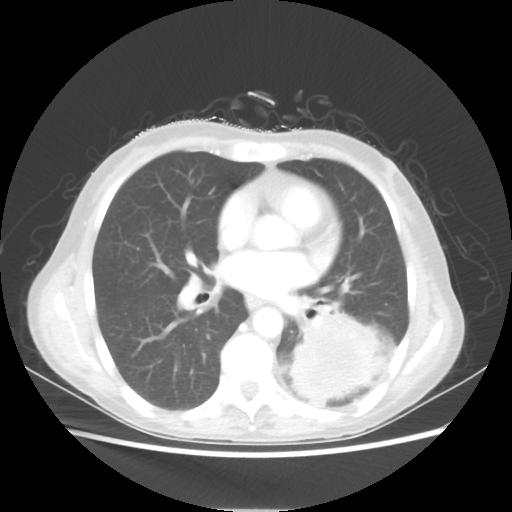
Chest CT, one axial slice. Slice 27 of 56 in the series (ordered by position). 80 kVp. Lung window (W 1500 / L -600 HU). 5 mm slice thickness. 512 × 512 image matrix. Female patient, age 53 years. From the clinical record (not read from this slice): clinical TNM (as recorded): T3 N0 M0.
Annotated regions visible in this slice (bounding box drawn by a radiologist):
- lung tumour (recorded histology: adenocarcinoma): box from (x=287, y=307) to (x=387, y=398) px